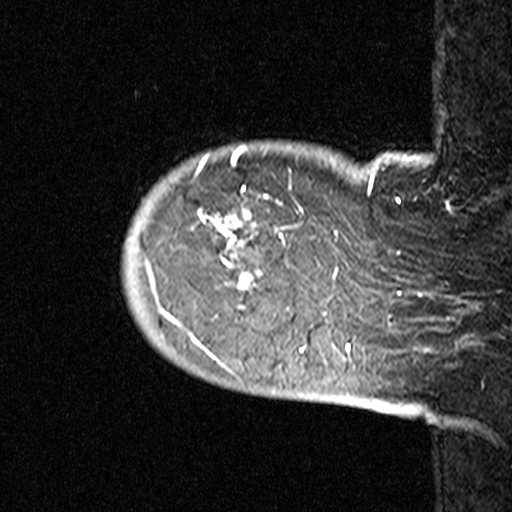
Breast MRI (dynamic contrast-enhanced), one sagittal slice; slice 5 of 44 in the series (ordered by position); dynamic contrast-enhanced study with each time point stored as its own series, time point 2 of 3 at this slice position (early post-contrast, ordered by acquisition time); 1.5 T; TE 4.5 ms, TR 11 ms; 512 × 512 image matrix, field of view 200 × 200 mm. Patient: female, 53 years. Case-level facts recorded for this patient, not image findings: setting: breast cancer imaged before/during neoadjuvant chemotherapy; receptor status: HR-positive, HER2-negative.
Annotated regions visible in this slice (semi-automatically segmented with operator editing):
- analysis volume of interest (the breast-tissue region the enhancement analysis was run in; not a lesion): bounding box [x1, y1, x2, y2] px = [120, 140, 311, 353]
- tumour enhancement mask (voxels above the 90 % enhancement threshold inside the analysis volume of interest): [147, 147, 303, 353]